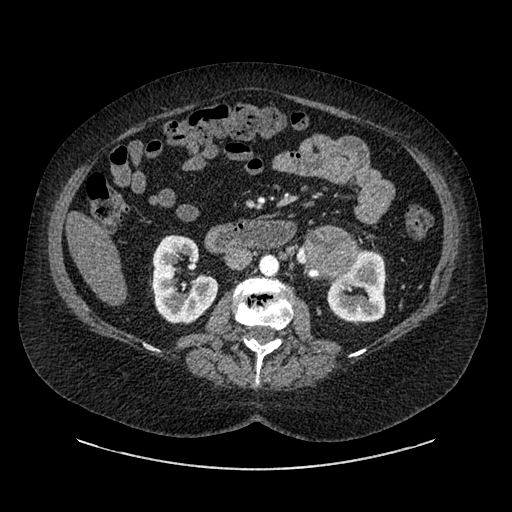
Contrast-enhanced abdominal CT, one axial slice. Slice 496 of 769 in the series (ordered by position). 120 kVp. Intravenous contrast given. Soft-tissue window (W 400 / L 40 HU). 512 × 512 image matrix. Patient: female, 61 years. From the clinical record (not read from this slice): diagnosis: adrenocortical carcinoma; tumour side: left adrenal; tumour size at pathology: 13 cm; Ki-67 index: 79 %; stage (as recorded): 2.
Annotated regions visible in this slice (semi-automatic segmentation, software-assisted and operator-edited):
- mass: bounding box <310,231,355,275> (left, top, right, bottom; pixels)